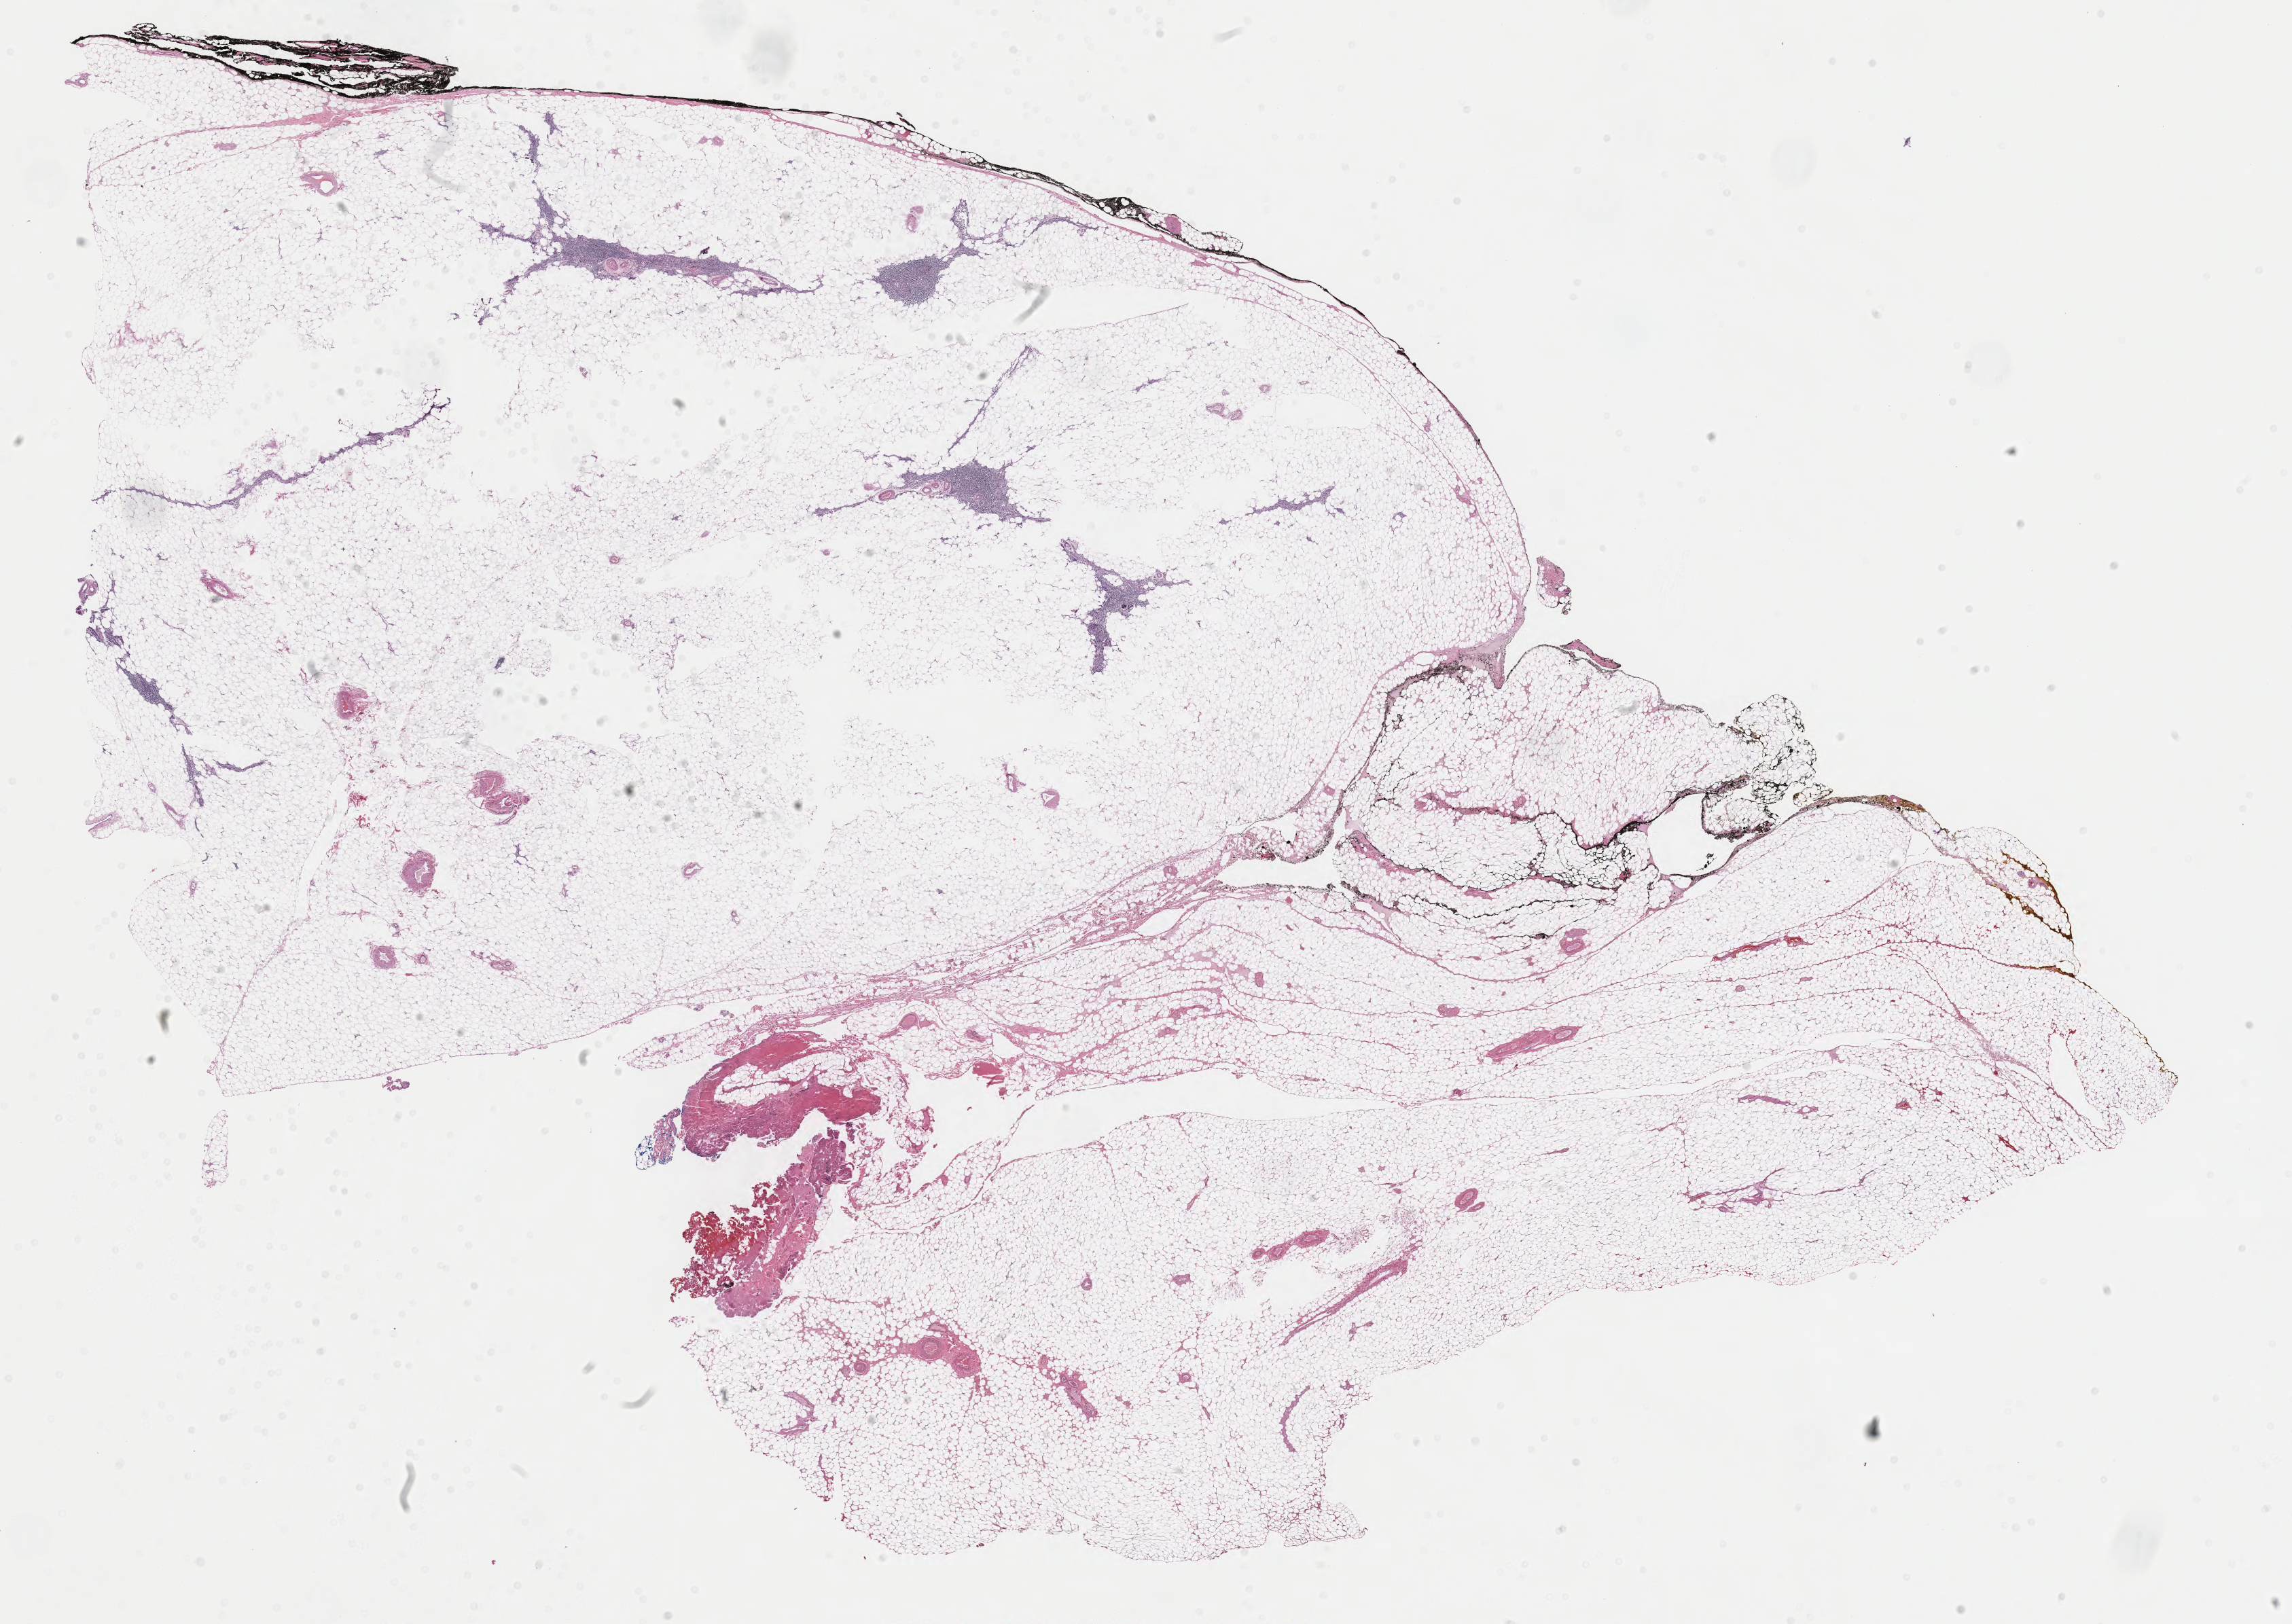
H&E whole-slide image, a low-resolution overview of the entire scanned area, about 26.8 x 19.0 mm (slide scanned at 40x), formalin-fixed paraffin-embedded (FFPE) diagnostic section, primary tumour sample from the thymus. Patient: male, age at initial diagnosis 52 years.
* pathologic diagnosis: Thymoma, type A, malignant